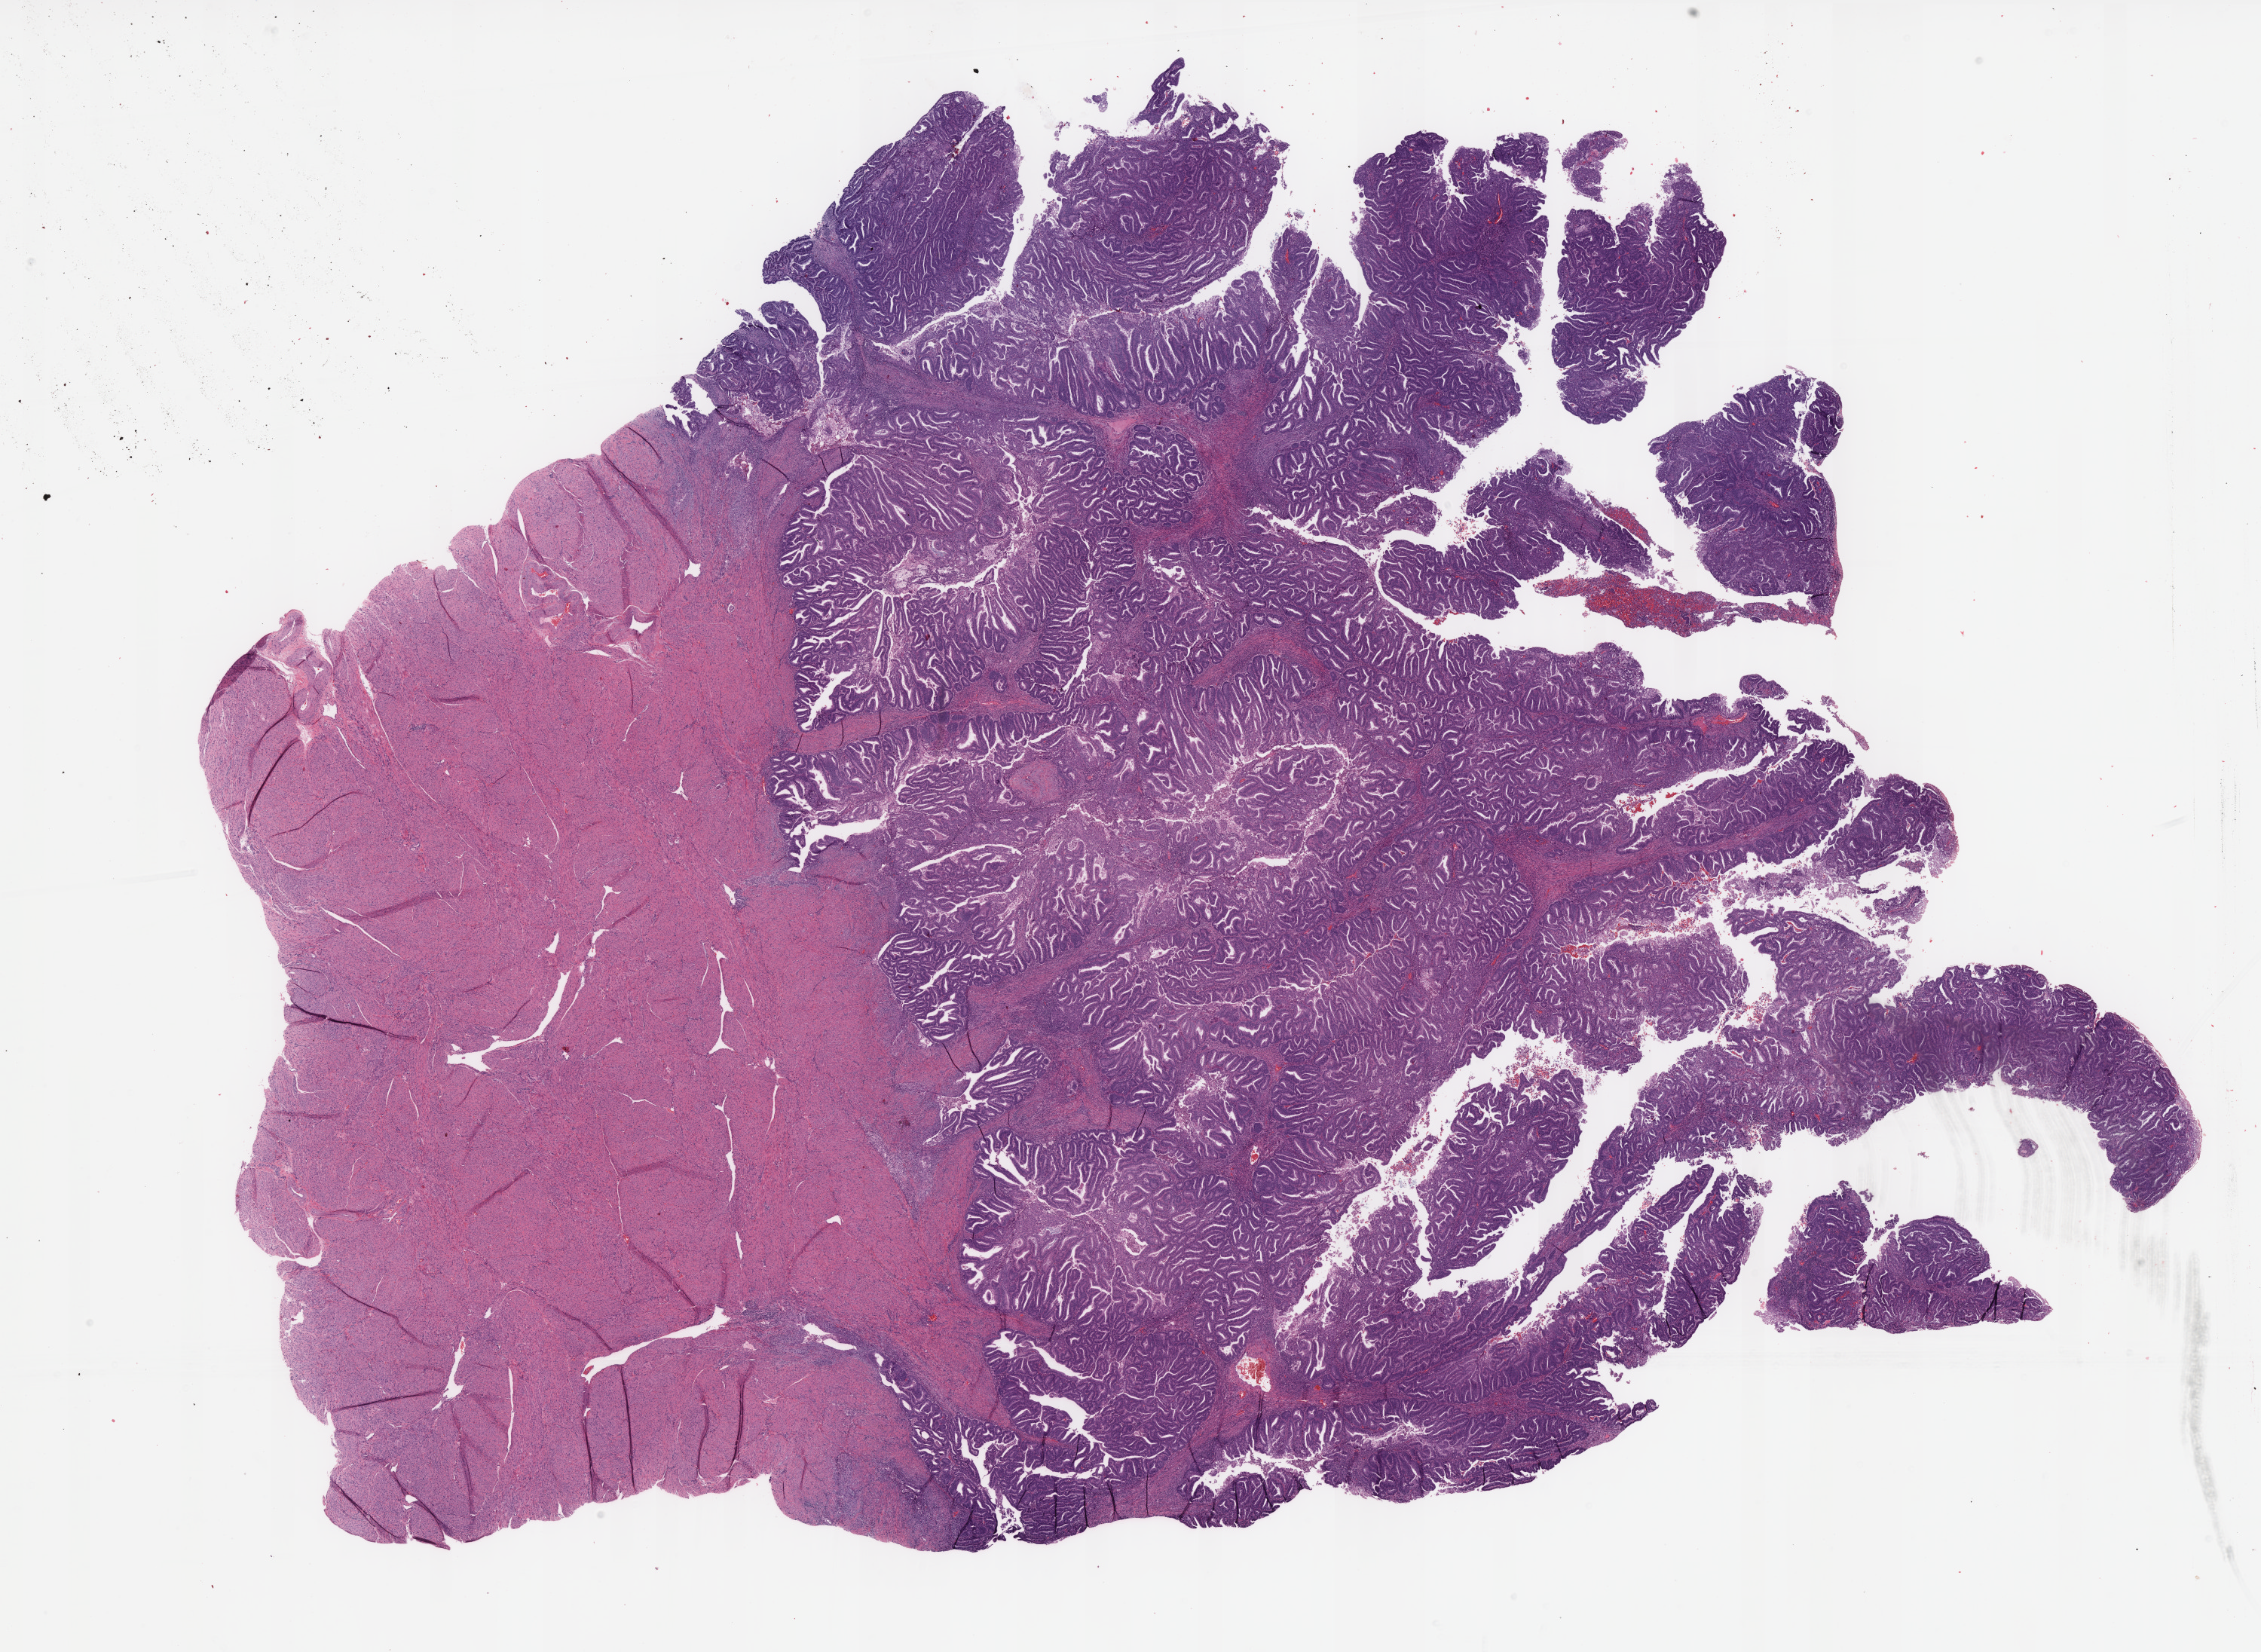
Digitized H&E tissue section (whole slide), a low-resolution overview of the entire scanned area, about 24.1 x 17.6 mm, formalin-fixed paraffin-embedded (FFPE) diagnostic section, uterus, primary tumour sample. Female patient; age at initial diagnosis 63 years.
Histologic diagnosis: Serous cystadenocarcinoma, NOS.